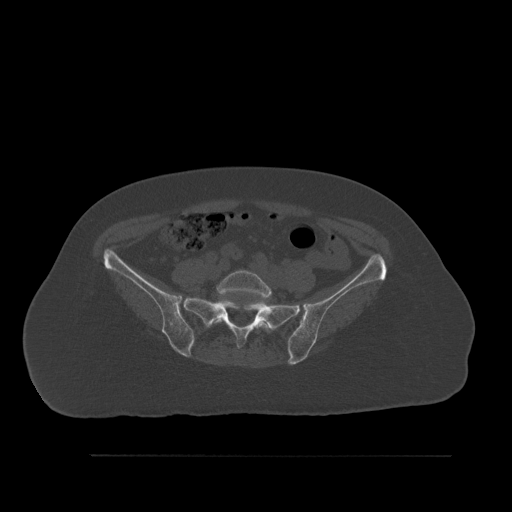
CT including the spine, one axial slice. Position 179 of 527 along the scan axis. Bone window (W 1800 / L 400 HU). 1.5 mm slice thickness. 512 × 512 image matrix, field of view 470 × 470 mm. Patient: female, 73 years. From the clinical record (not read from this slice): primary cancer: breast.
Structures marked on this image (semi-automatically segmented with operator editing):
- L5 vertebra: box from (x=212, y=270) to (x=273, y=333) px